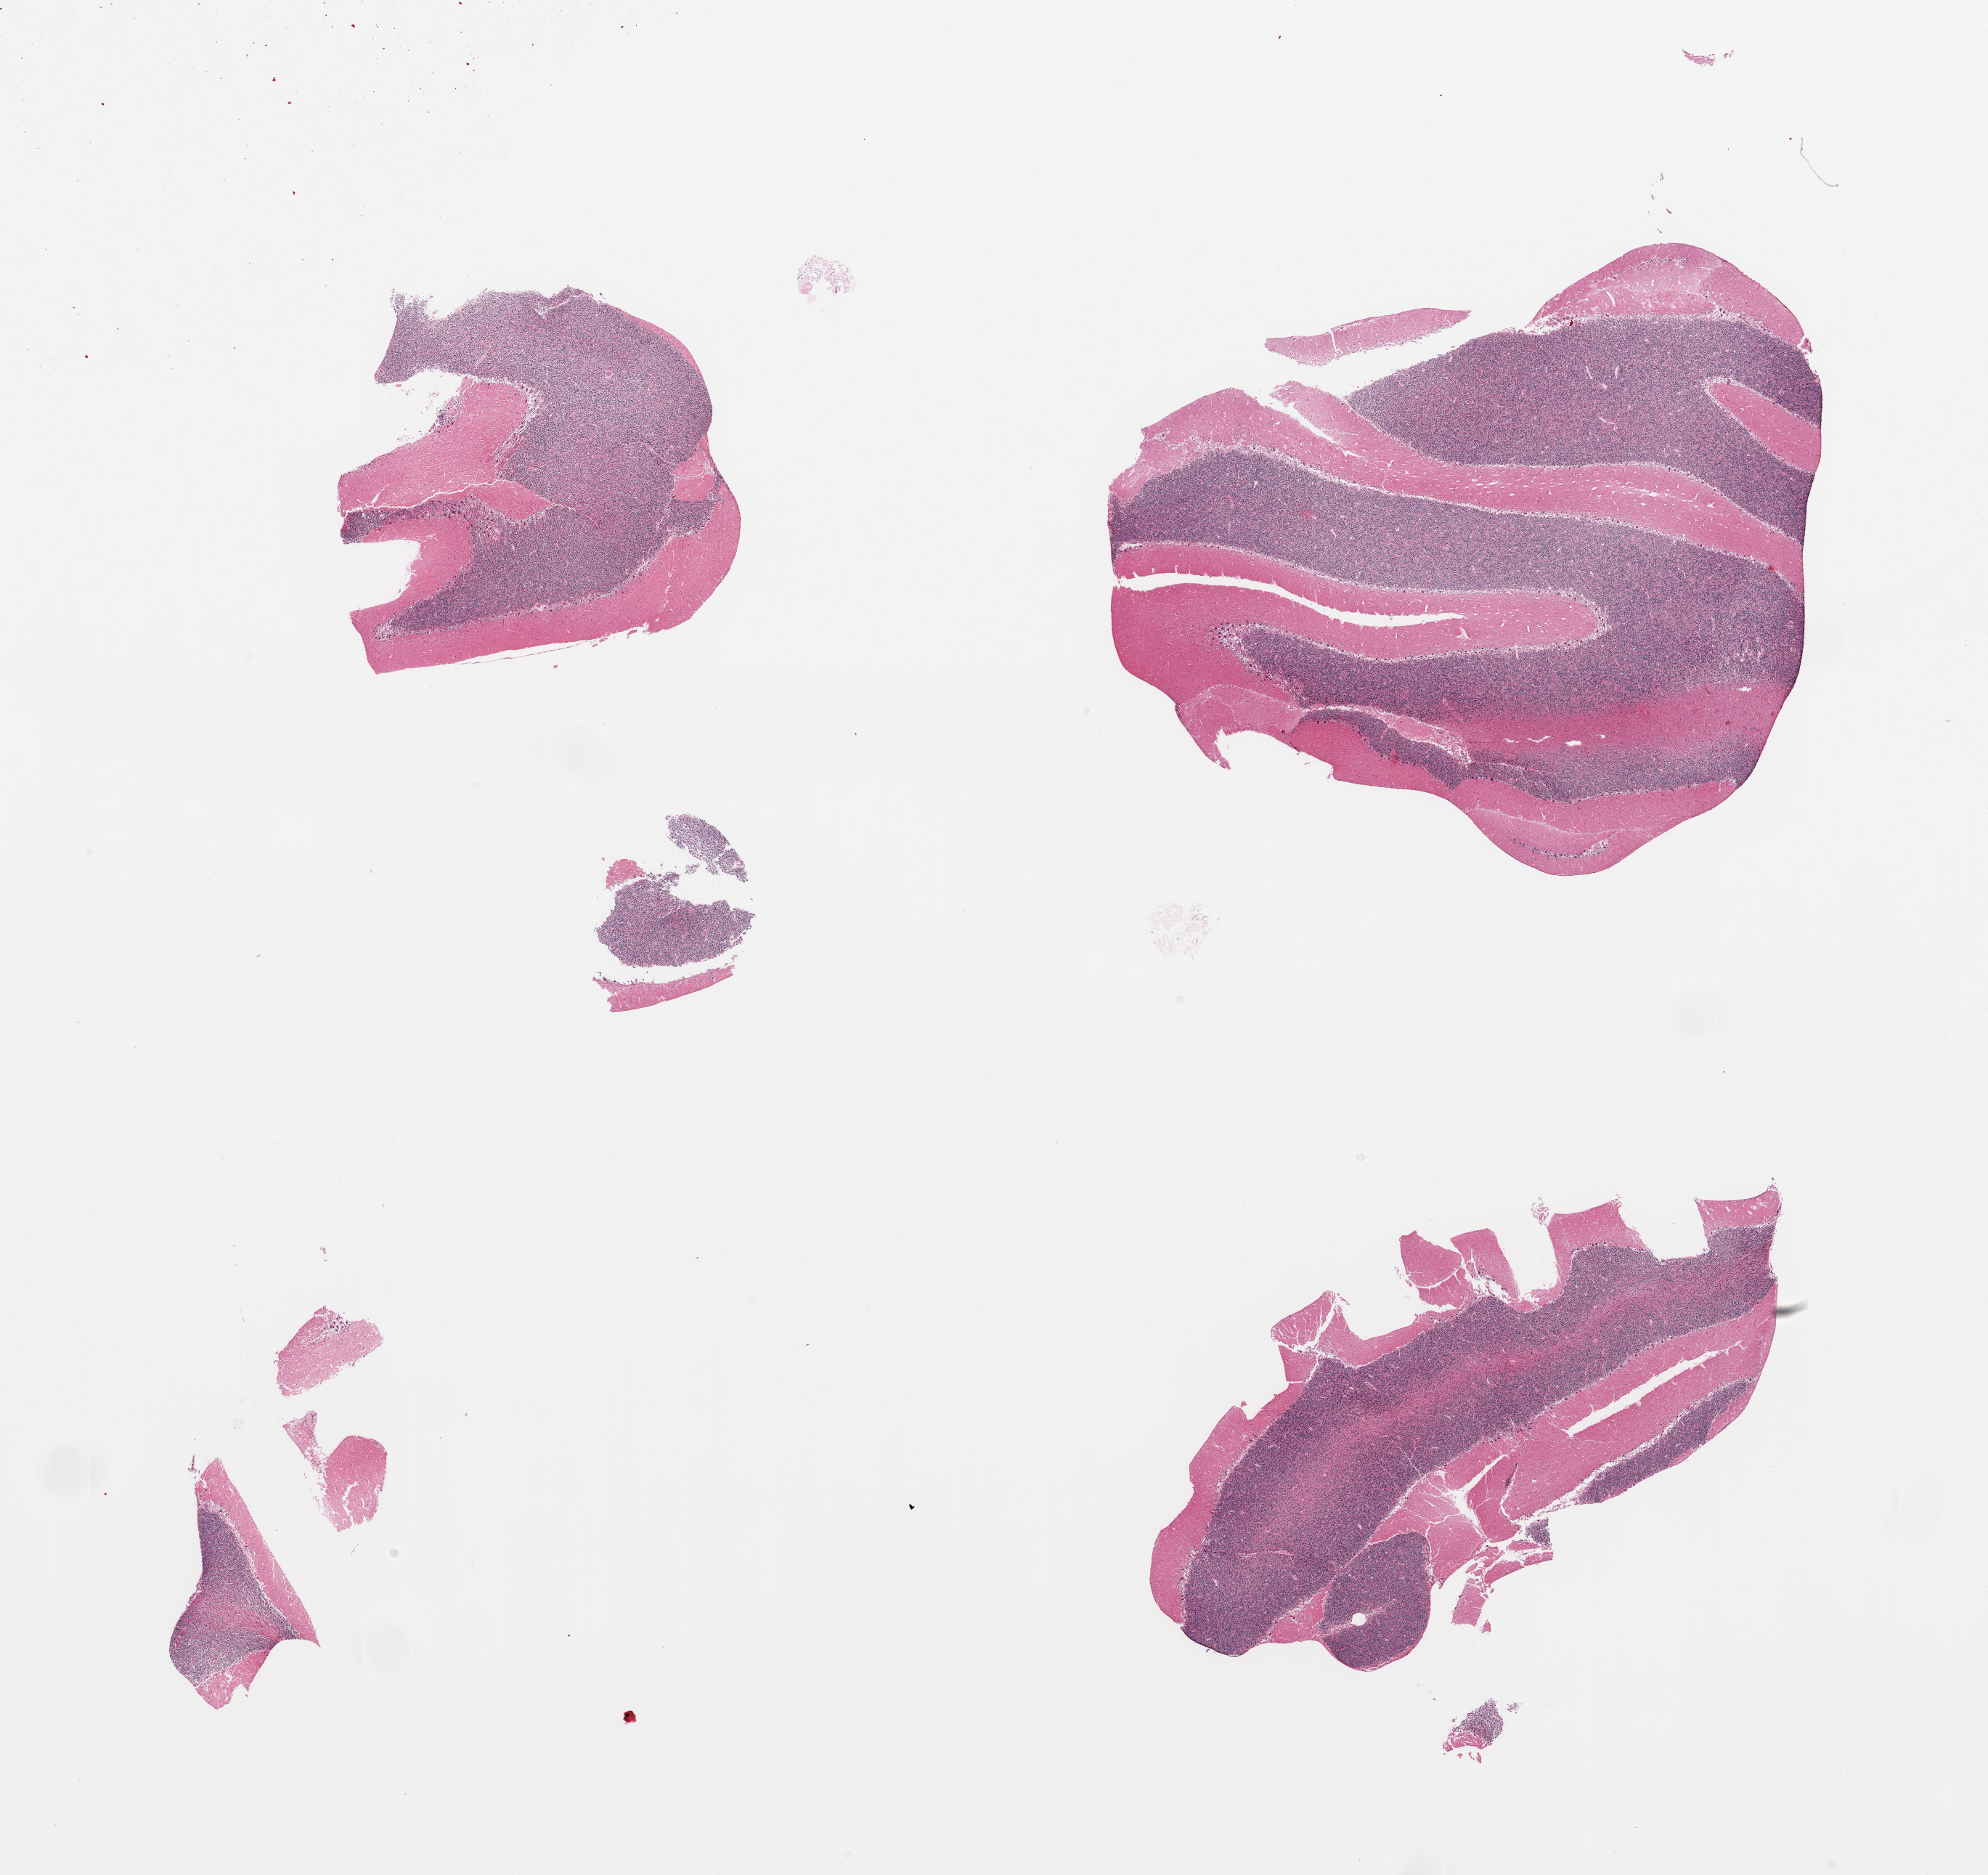
H&E whole-slide image — shown as a low-resolution overview of the whole scanned area (about 21.7 x 20.4 mm, slide scanned at 20x); PAXgene-fixed paraffin-embedded (PFPE) section; section of cerebellum (target tissue); tissue donor sample. Donor sex: male.
• review note (as recorded): 3 pieces, no abnormalities